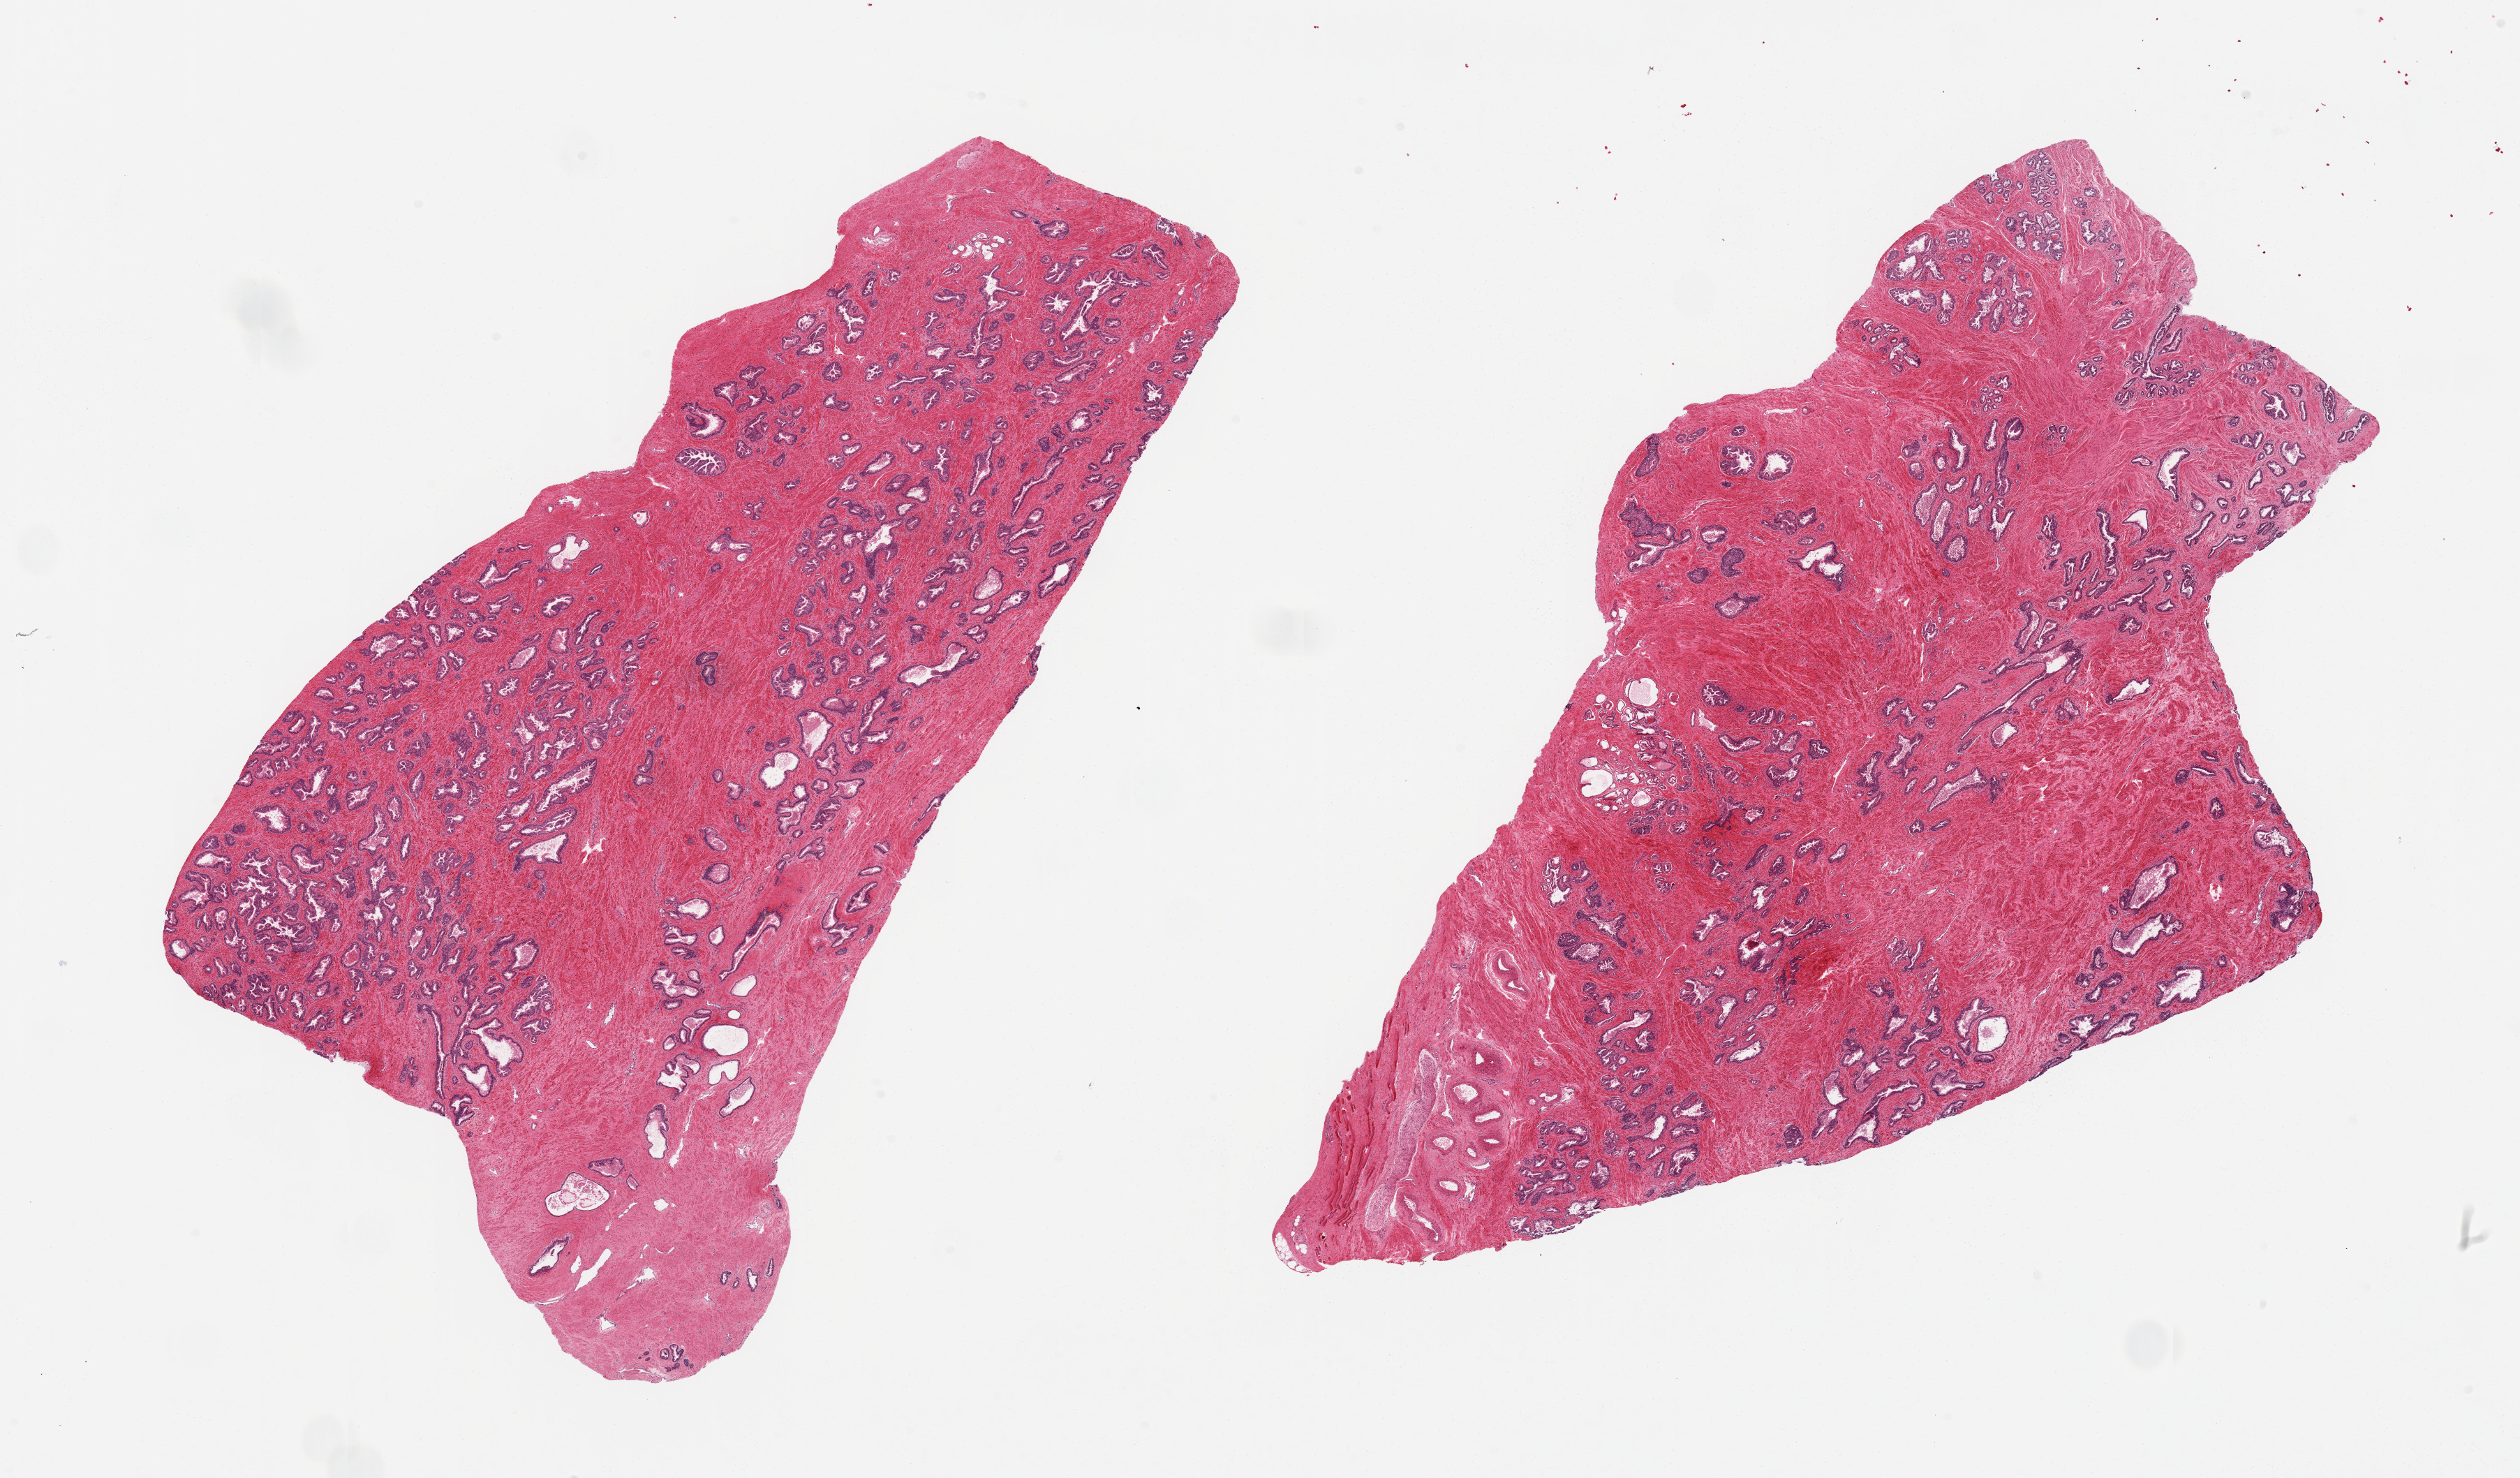
H&E whole-slide image, low-resolution overview of the scanned area, about 28.5 x 16.7 mm (from a 20x scan), PAXgene-fixed paraffin-embedded (PFPE) section, sampled site (target tissue): prostate, donor tissue sample. Donor: male.
Reviewer comment on this tissue sample: 2 pieces; well preserved glands without hyperplasia.